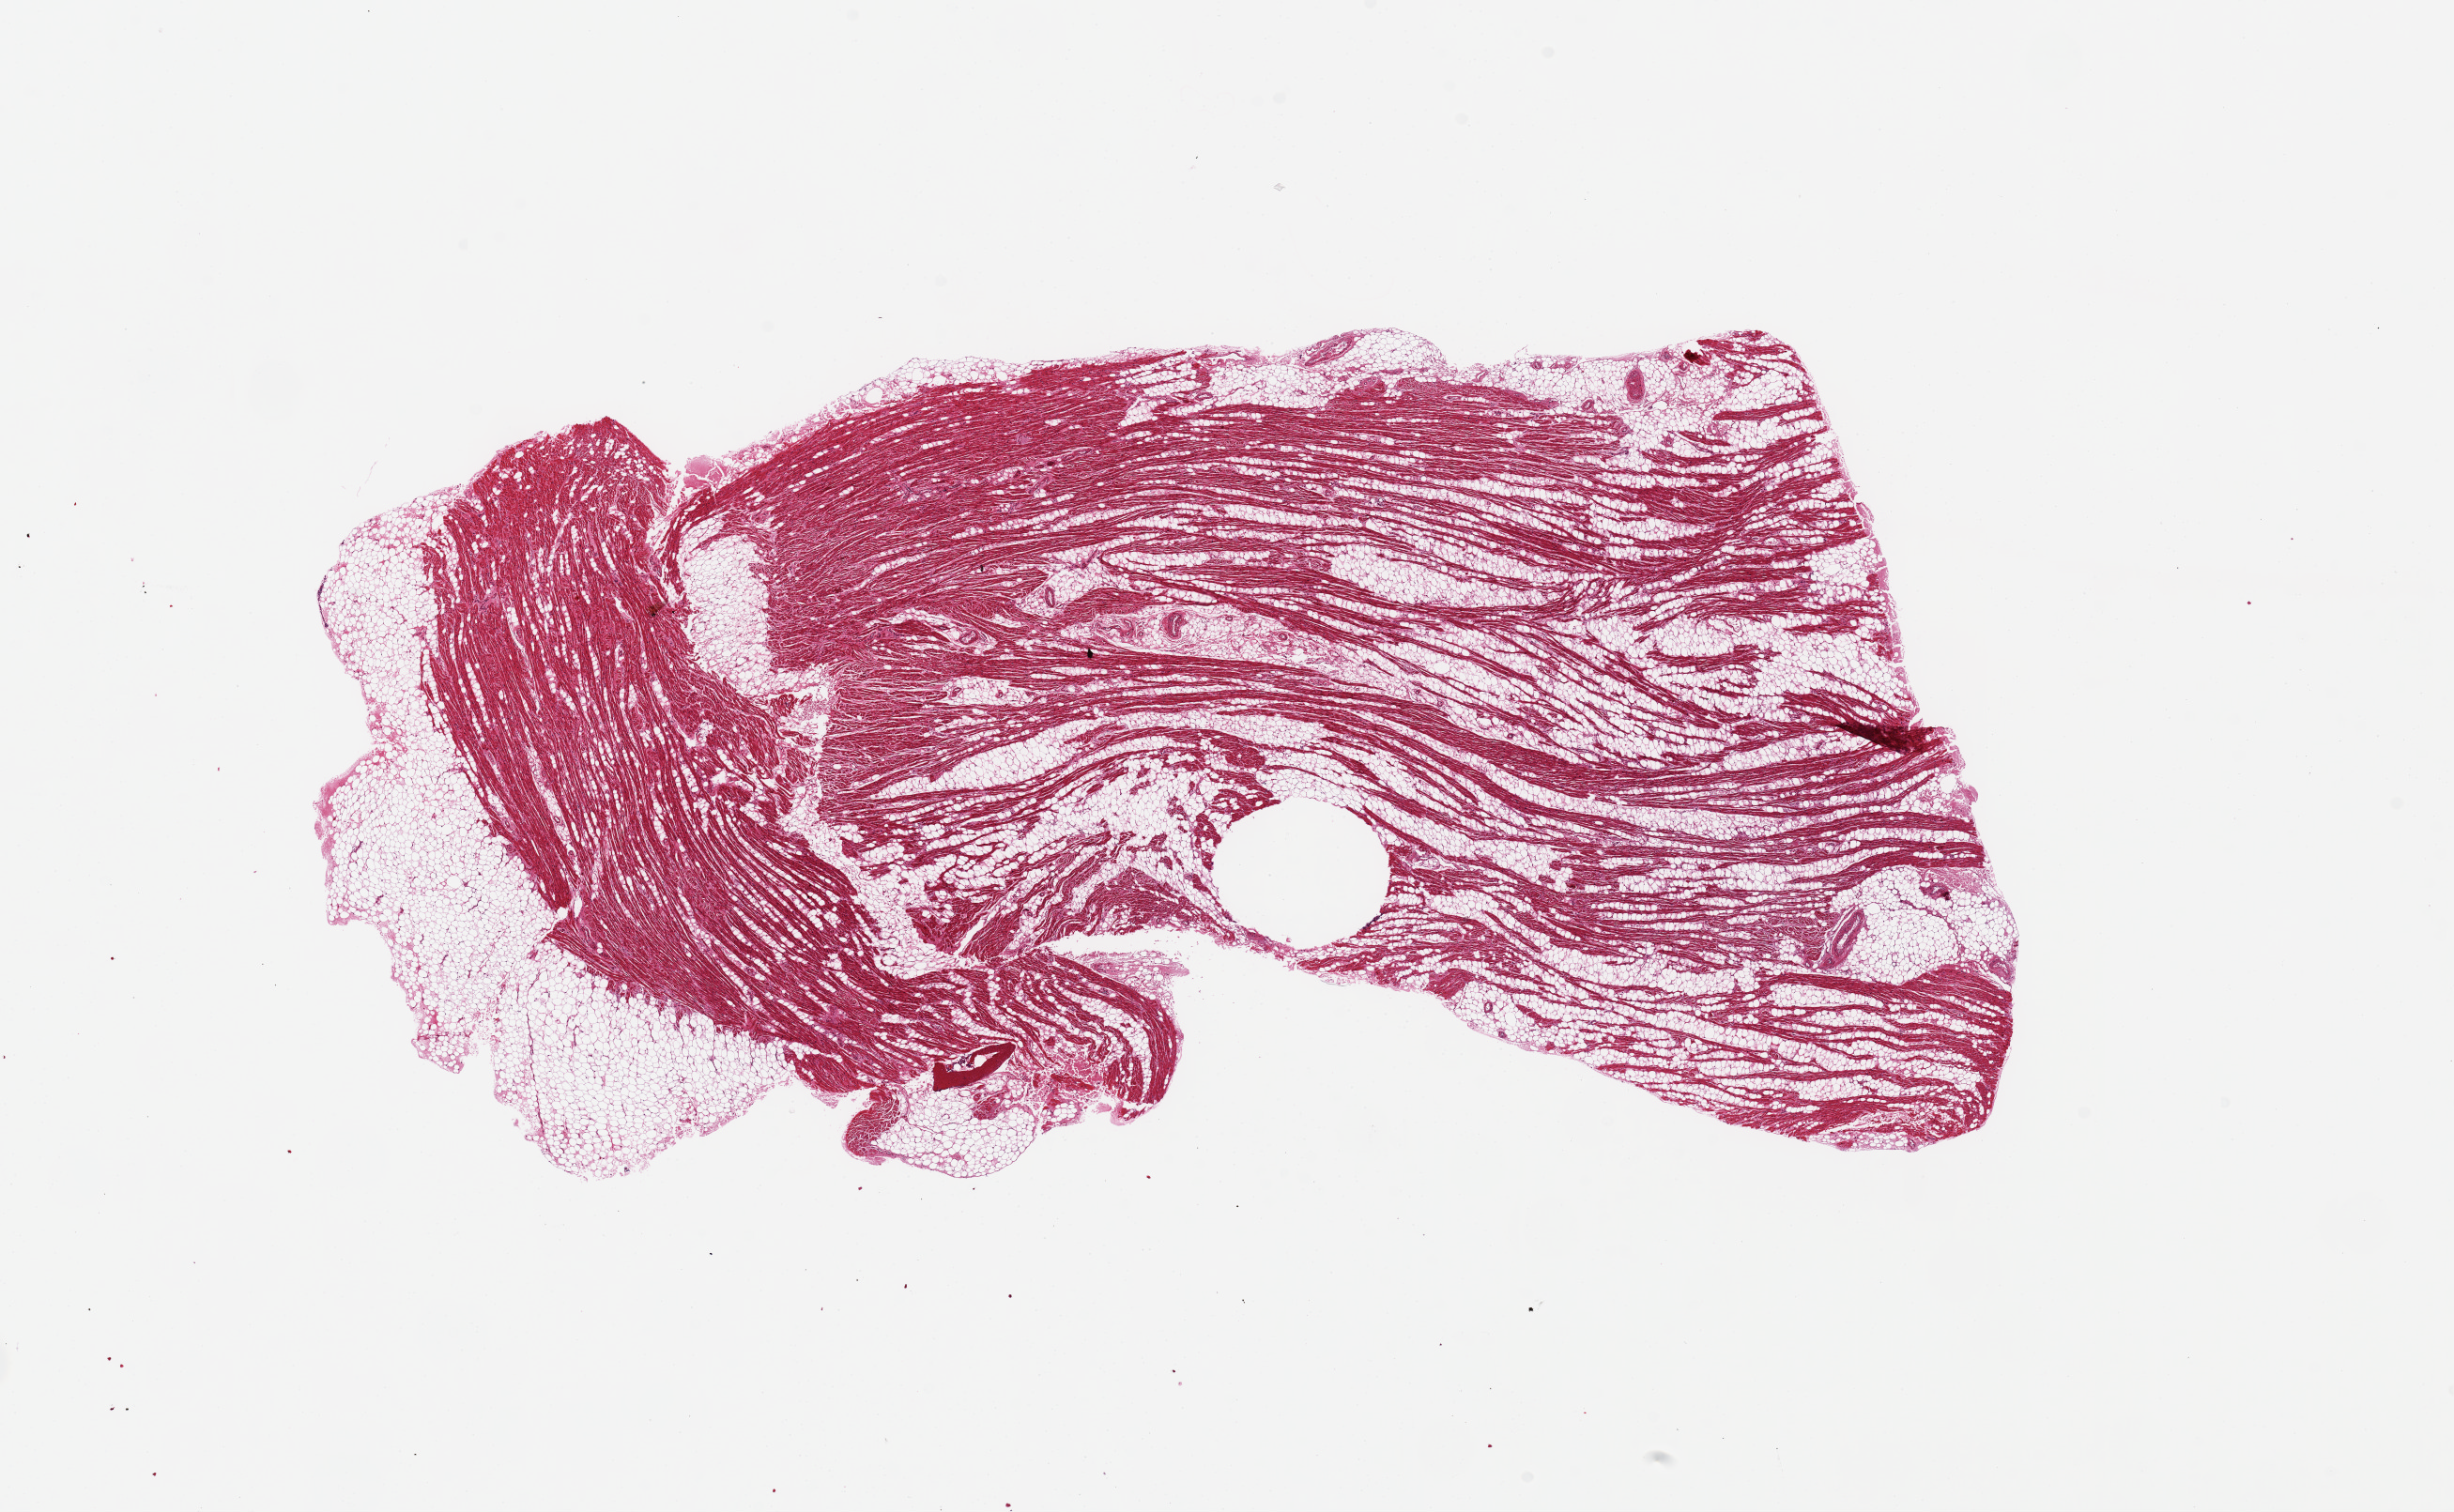
Whole-slide image, H&E stain, brightfield — low-resolution overview of the scanned area, about 20.7 x 12.7 mm (slide scanned at 20x). PAXgene-fixed paraffin-embedded (PFPE) section. Target tissue: heart. Donor tissue sample. Donor sex: female.
Pathologist's review note for this sample: Fatty infiltration of myocardium; 1 piece 12x5 mm.